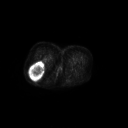
FDG PET of an extremity soft-tissue mass (from a PET/CT study), one axial slice. Slice 40 of 267 in the series (ordered by position). 3.27 mm slice thickness. 128 × 128 image matrix, field of view 700 × 700 mm. Patient: female, 70 years. Case-level facts recorded for this patient, not image findings: histological type: synovial sarcoma; grade: intermediate; site of the primary tumour: right buttock.
Structures marked on this image (expert contour drawn on MRI and transferred to this co-registered scan by the dataset authors):
- gross tumour volume including surrounding oedema: bounding box [x1, y1, x2, y2] px = [29, 61, 44, 80]
- gross tumour volume (mass): [29, 61, 44, 80]